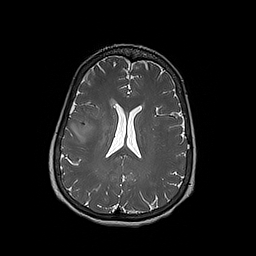
Brain MRI from a brain-tumour surgery series, one axial slice; position 83 of 192 along the scan axis; 1 mm slice thickness; 256 × 256 image matrix, field of view 250 × 250 mm. From the clinical record (not read from this slice): histopathology: Oligodendroglioma; WHO grade: 3; IDH mutation: yes.
Outlined on this slice (outlined manually by an expert reader):
- tumour: bounding box [x1, y1, x2, y2] px = [73, 118, 93, 133]